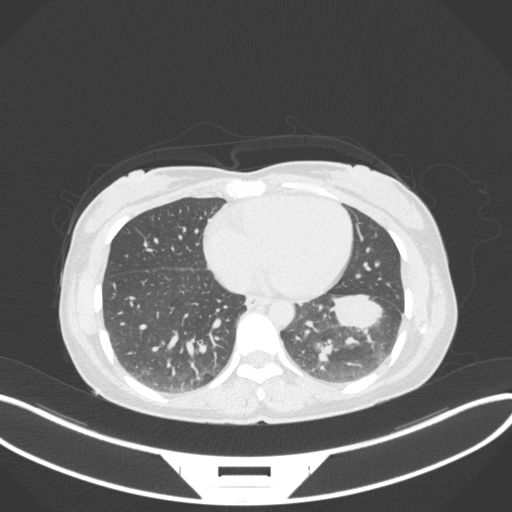
Chest CT, one axial slice; lung window (W 1500 / L -600 HU); 1 mm slice thickness; 512 × 512 image matrix. Patient: female, 41 years. Case-level facts recorded for this patient, not image findings: clinical TNM (as recorded): T2a N3 M1b.
Structures marked on this image (bounding box drawn by a radiologist):
- lung tumour (recorded histology: adenocarcinoma): box from (x=328, y=293) to (x=386, y=334) px